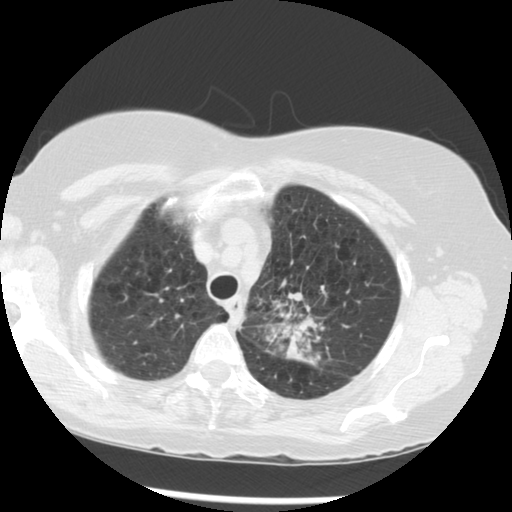
Axial slice from a low-dose chest CT screening exam, third screening round (two years after baseline), lung window (W 1500 / L -600 HU), standard (soft-tissue) reconstruction kernel (STANDARD), 512 × 512 image matrix, field of view 330 × 330 mm. Female, age 70 years at enrolment. Current smoker at enrolment.
Expert reader's lesion annotation, bounding box <256,279,352,368> (left, top, right, bottom; pixels). The exam's reader record, not a measurement of the box and not confirmed to be the same lesion: non-calcified nodule or mass ≥4 mm, left upper lobe, 32 × 26 mm, spiculated (stellate) margins, soft tissue attenuation, pre-existing on the prior screen: yes; interval growth: yes. Official screen result: positive, other. Participant outcome: lung cancer diagnosed 24 days after this screen — neoplasm, malignant, left upper lobe, stage IIIB (AJCC 6th edition), 40 mm at pathology.